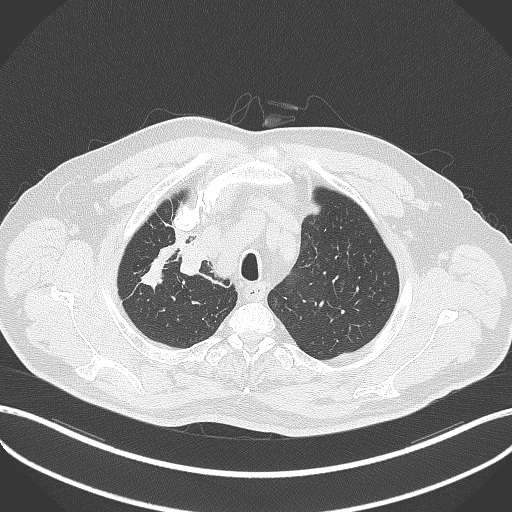
Chest CT, one axial slice. Slice 322 of 411 in the series (ordered by position). Reconstruction kernel B70f. Lung window (W 1500 / L -600 HU). 512 × 512 image matrix, field of view 400 × 400 mm. Male patient, age 60 years. From the clinical record (not read from this slice): clinical TNM (as recorded): T1b N1 M0.
Outlined on this slice (rectangle marked by the reading radiologist):
- lung tumour (recorded histology: squamous cell carcinoma): bounding box (x1, y1, x2, y2) in pixels: (177, 236, 211, 278)